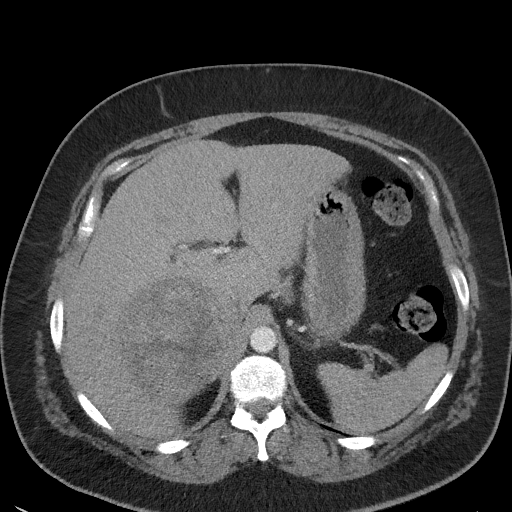
Contrast-enhanced abdominal CT, one axial slice; position 37 of 56 along the scan axis; reconstruction kernel I41f/3; 120 kVp; soft-tissue window (W 400 / L 40 HU); 512 × 512 image matrix, field of view 373 × 373 mm. Female patient, age 35 years. Case-level facts recorded for this patient, not image findings: diagnosis: adrenocortical carcinoma; tumour side: right adrenal; tumour size at pathology: 15 cm; Ki-67 index: 40 %; stage (as recorded): 2.
Structures marked on this image (semi-automatically segmented with operator editing):
- mass: bounding box <124,278,228,398> (left, top, right, bottom; pixels)